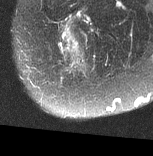
MRI of an extremity soft-tissue mass, one axial slice. Position 18 of 77 along the scan axis. T2-weighted fat-saturated. MR volume resampled by the dataset authors to the PET/CT grid (not the native acquisition matrix). 3.27 mm slice thickness. 153 × 156 image matrix, field of view 149 × 152 mm. Female patient. From the clinical record (not read from this slice): histological type: synovial sarcoma; grade: intermediate; site of the primary tumour: right buttock.
Annotated regions visible in this slice (expert contour drawn on MRI and transferred to this co-registered scan by the dataset authors):
- gross tumour volume including surrounding oedema: bounding box (x1, y1, x2, y2) in pixels: (58, 22, 86, 71)